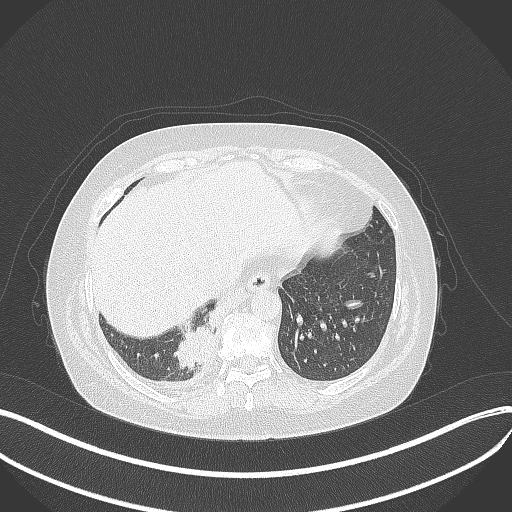
Chest CT, one axial slice; slice 90 of 381 in the series (ordered by position); reconstruction kernel B70f; lung window (W 1500 / L -600 HU); 512 × 512 image matrix, field of view 400 × 400 mm. Patient: female, 56 years. From the clinical record (not read from this slice): clinical TNM (as recorded): T2b N1 M0; histopathological grade: G3.
Structures marked on this image (bounding box drawn by a radiologist):
- lung tumour (recorded histology: small cell carcinoma): box from (x=169, y=314) to (x=219, y=370) px